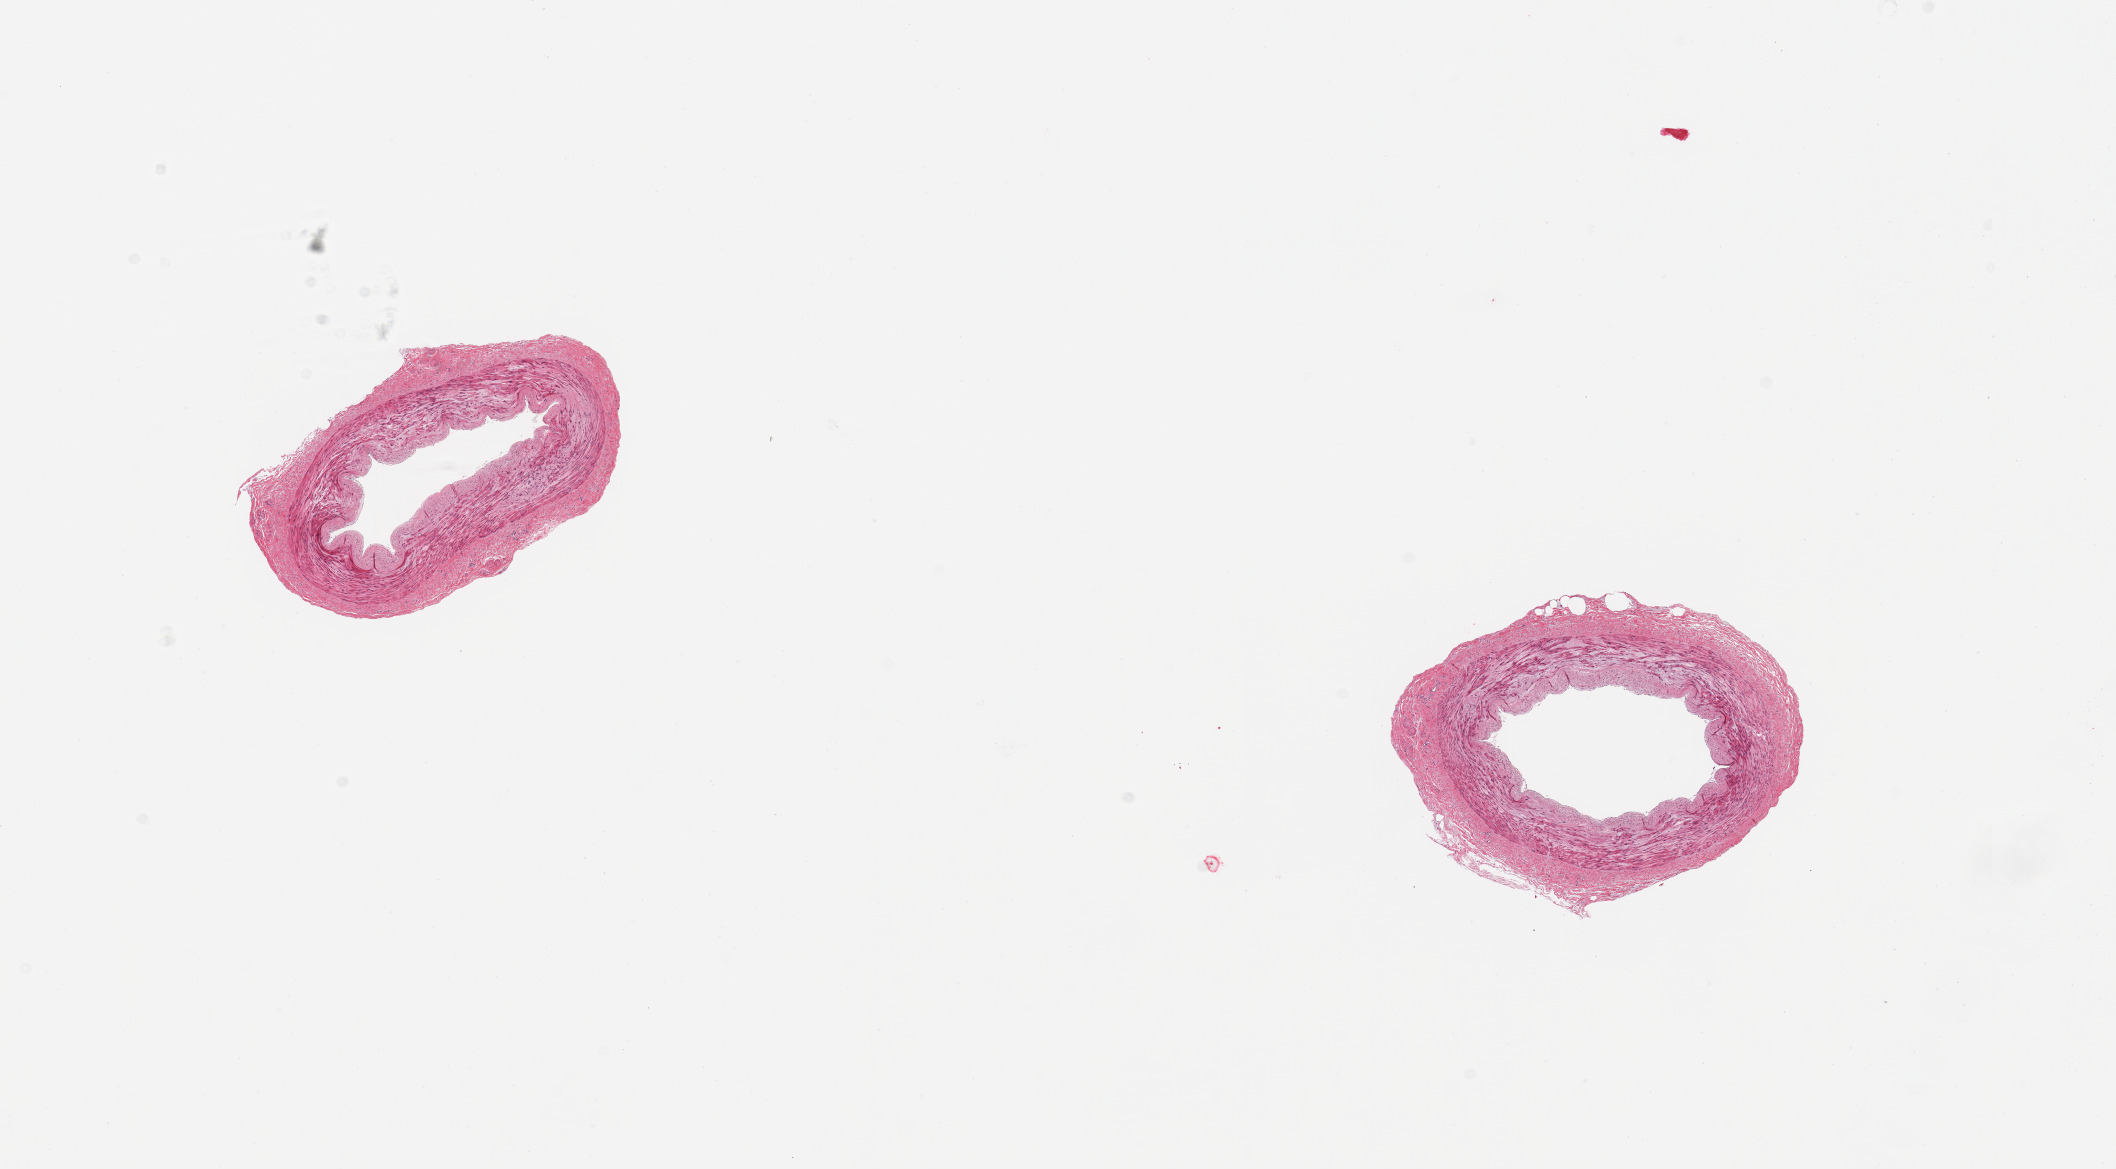
Digitized haematoxylin and eosin-stained section, brightfield, whole scanned area (about 16.7 x 9.2 mm, slide scanned at 20x) shown as a low-resolution overview. PAXgene-fixed paraffin-embedded (PFPE) section. Section of tibial artery (target tissue). Donor tissue sample. Donor: male.
Reviewer comment on this tissue sample: 2 pieces; well trimmed, no plaques.